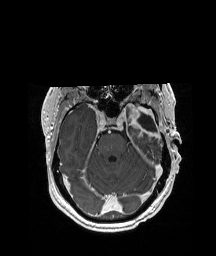
Brain MRI from a brain-tumour surgery series, one axial slice; position 136 of 208 along the scan axis; T1-weighted post-contrast; 1 mm slice thickness; 216 × 256 image matrix, field of view 228 × 270 mm. From the clinical record (not read from this slice): histopathology: Glioblastoma; WHO grade: 4; IDH mutation: no; tumour location: Left Anterior/Superior Temporal.
Structures marked on this image (outlined manually by an expert reader):
- previous resection cavity: bounding box [x1, y1, x2, y2] px = [135, 107, 157, 133]
- tumour: [123, 100, 158, 134]